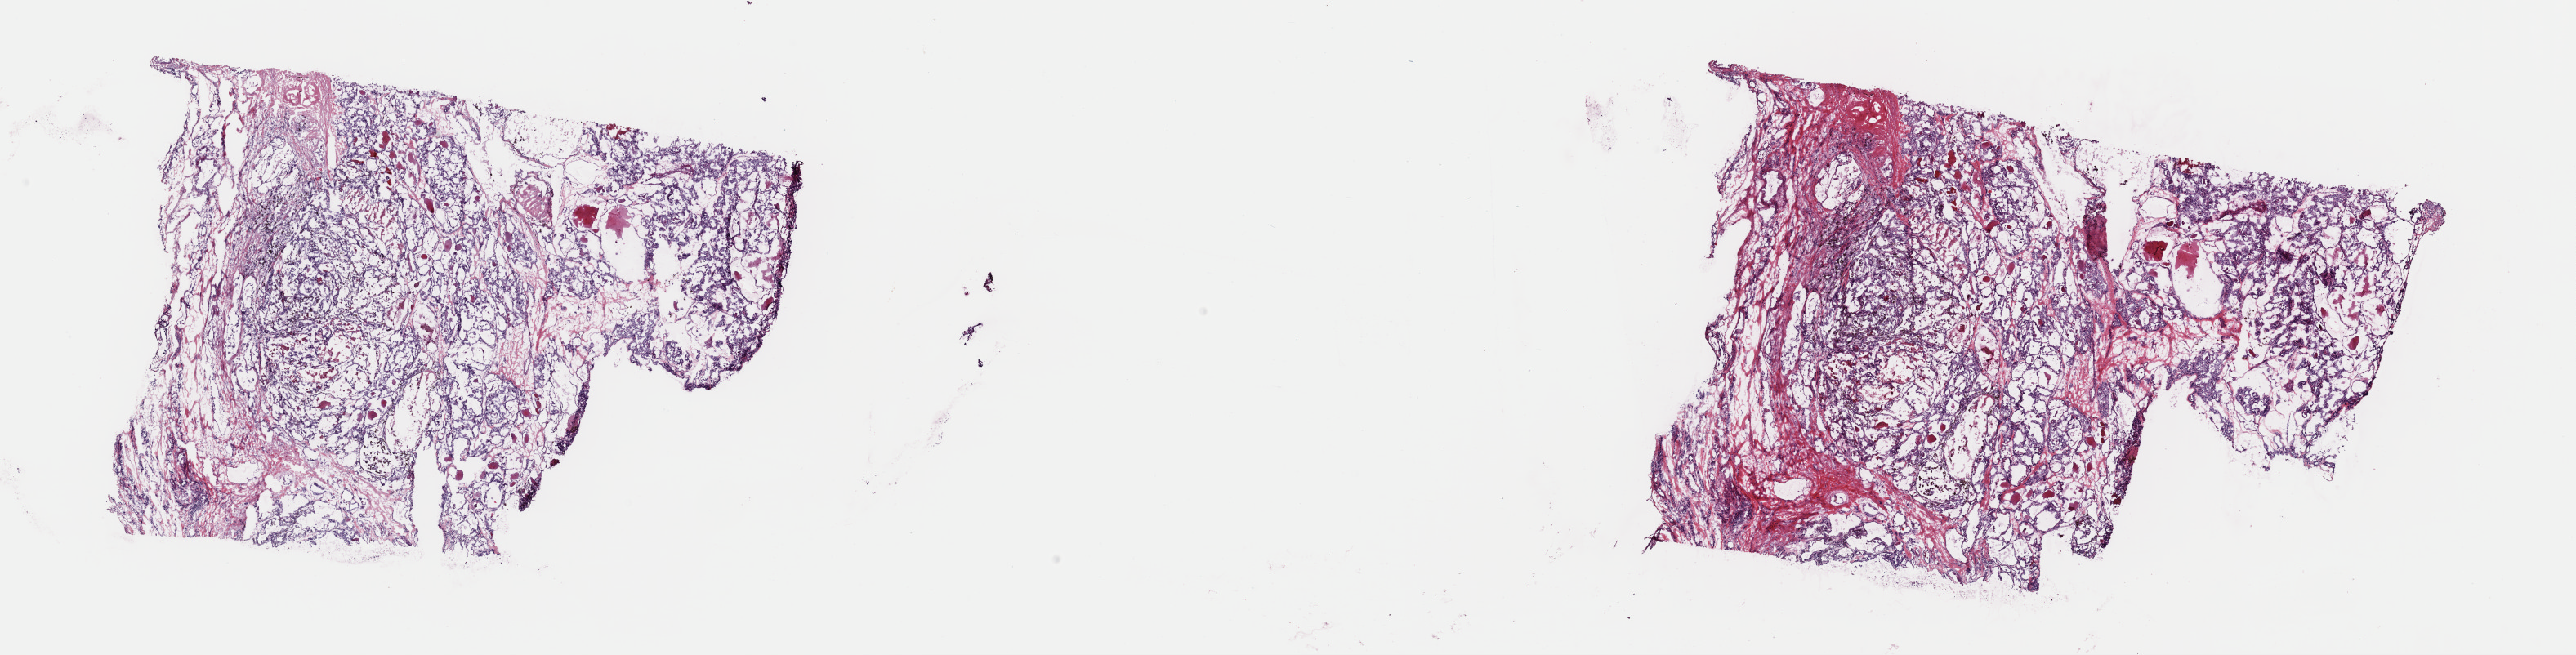
Digitized Hematoxylin and eosin (H&E) stained tissue section (whole slide), low-resolution overview of the scanned area, about 24.9 x 6.3 mm (acquisition: 40x scan). Frozen section. Thyroid, primary tumour sample. Male, age 36 years at initial diagnosis. Composition of this section per pathologist review: tumour cells 80%, tumour nuclei 100%, normal cells 0%, stromal cells 20%, necrosis 0%. Inflammatory infiltration, as recorded: lymphocyte infiltration 1%, monocyte infiltration 1%, neutrophil infiltration 0%.
* diagnosis: Papillary carcinoma, follicular variant (thyroid gland)
* laterality: midline
* AJCC pathologic stage: I (7th edition)
* lymph nodes positive (case pathology): 0 of 1 examined